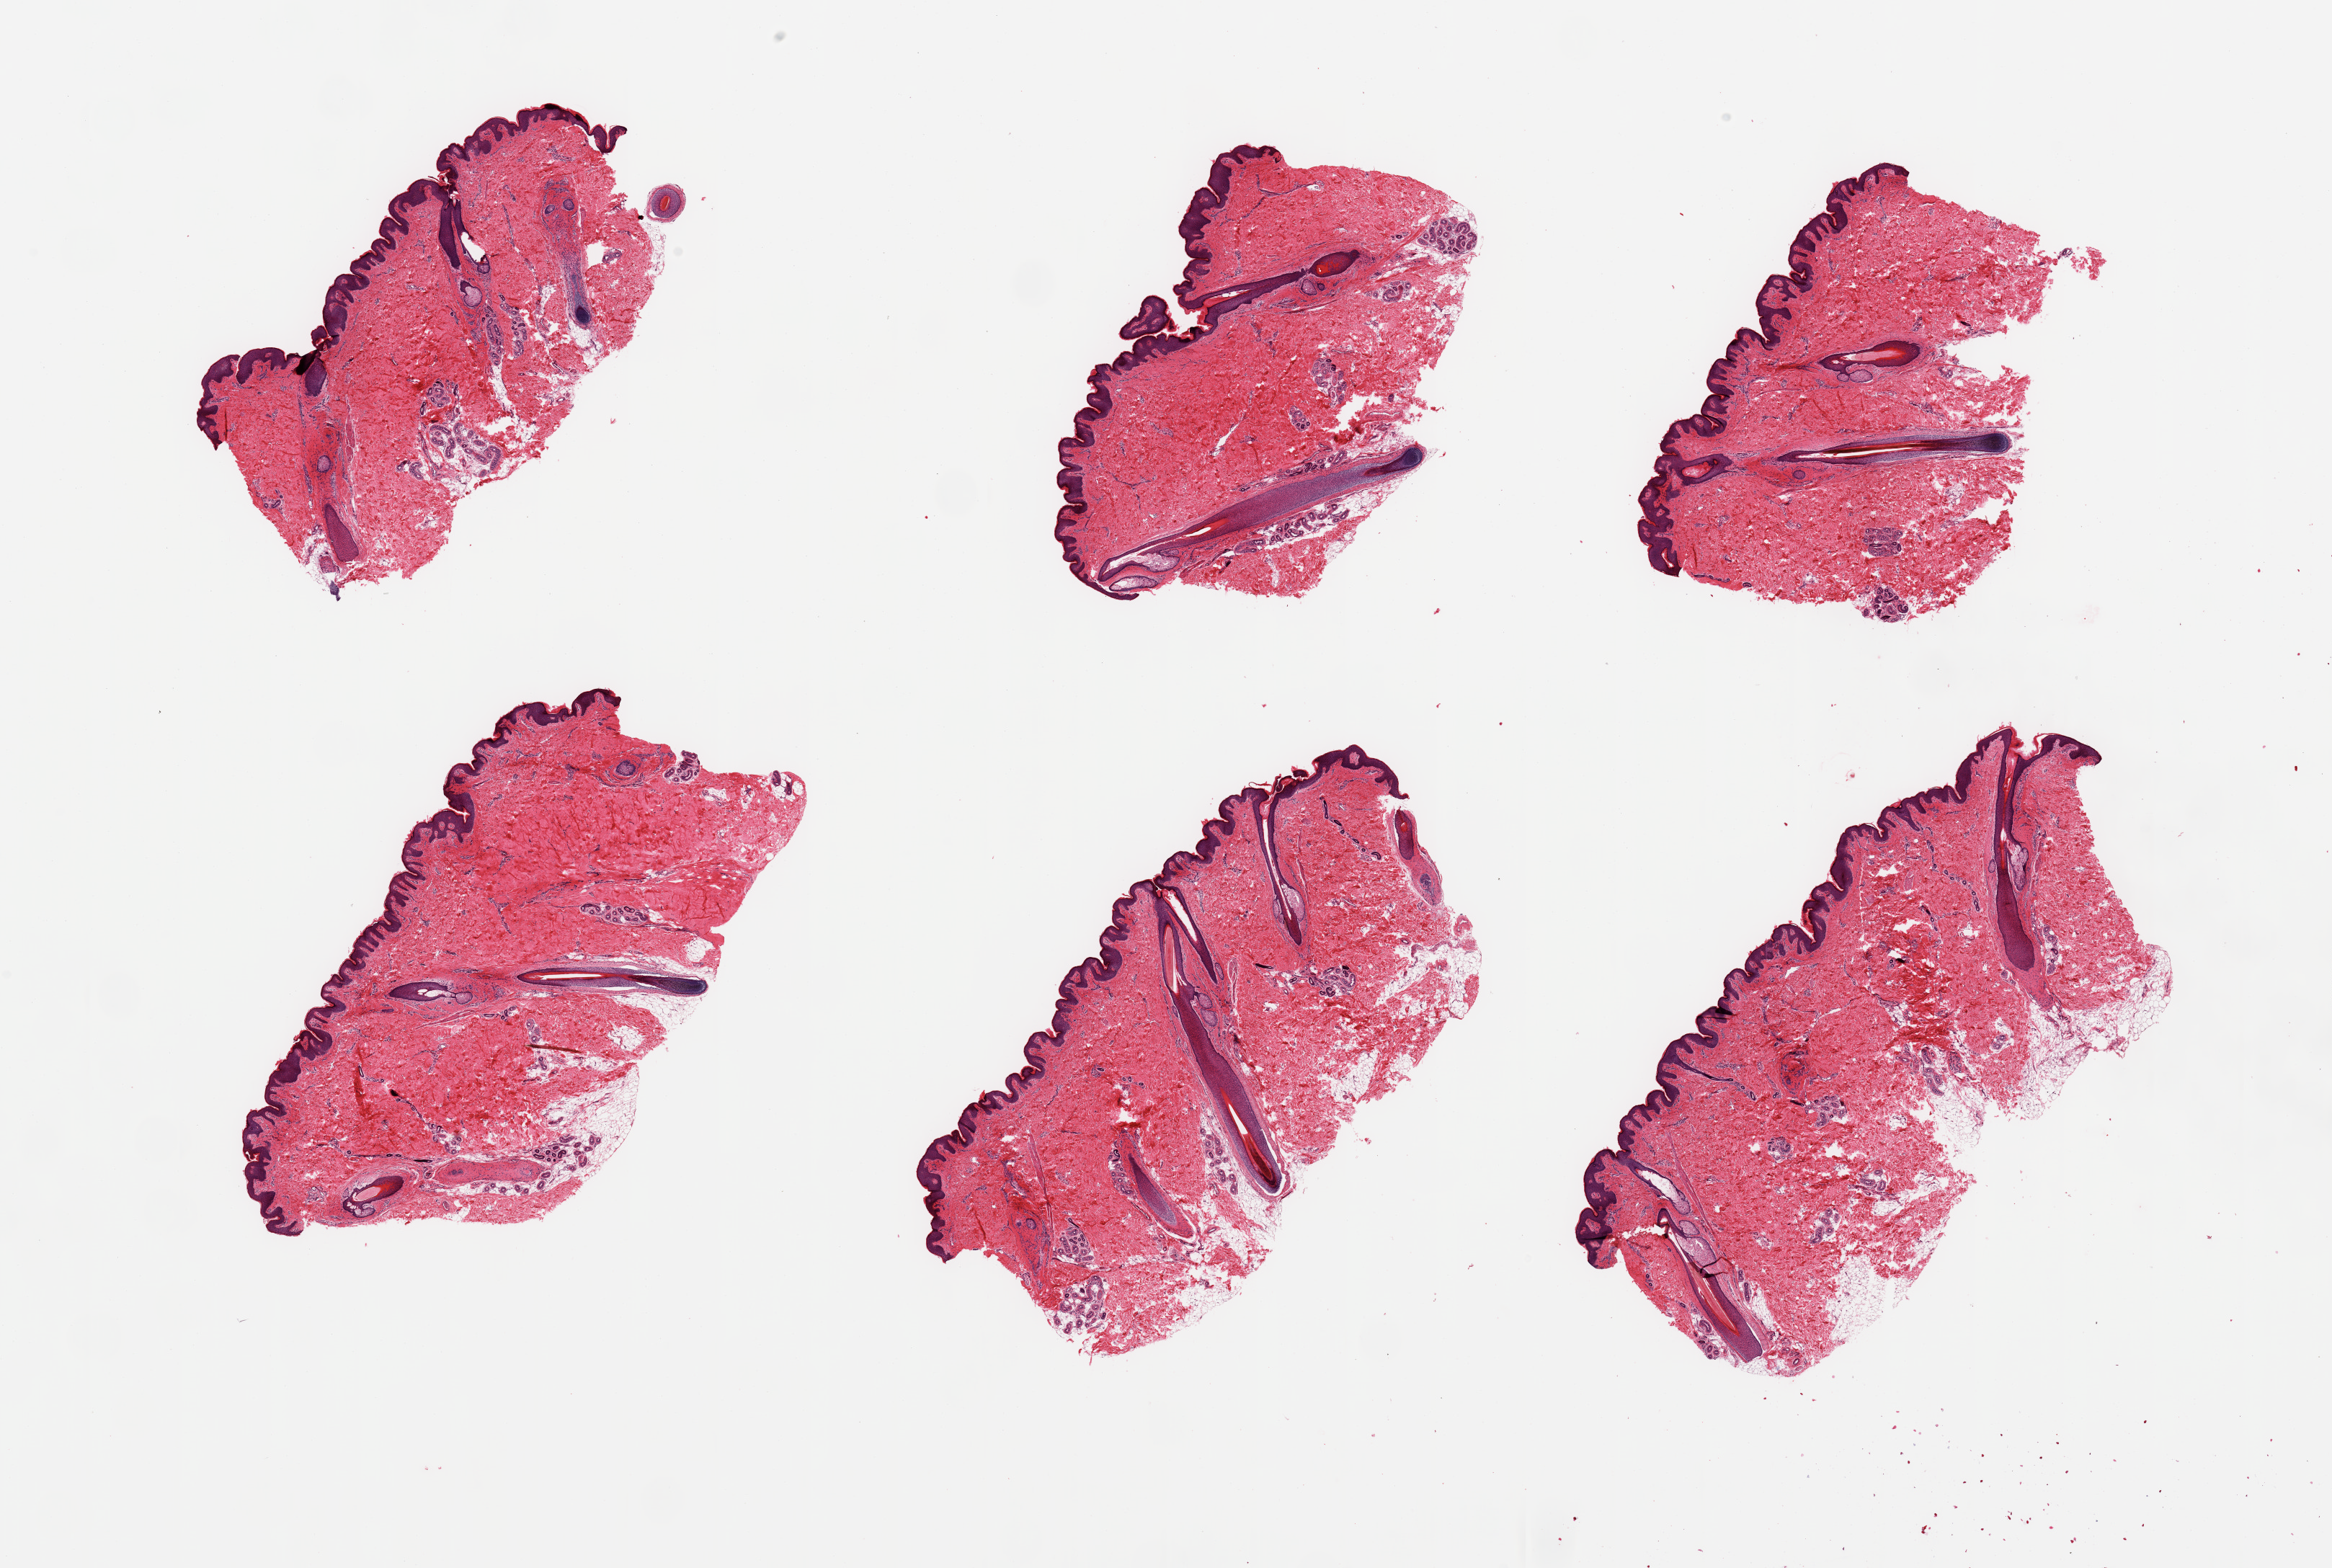
Whole-slide image, haematoxylin and eosin stain, low-resolution overview of the scanned area, about 25.6 x 17.2 mm (from a 20x scan). PAXgene-fixed, paraffin-embedded tissue. Section of skin of suprapubic region (target tissue). Donor tissue sample. Donor: male.
• reviewer comment on this tissue sample: 6 pieces; squamous epithelium is ~50-60 microns; minimal adherent dermal fat